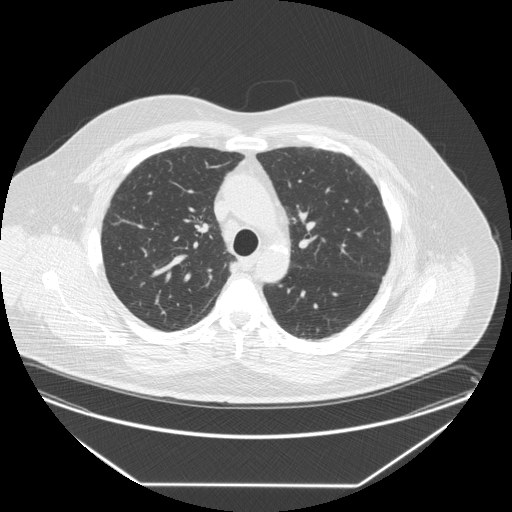
Low-dose screening chest CT, one axial slice; lung window (W 1500 / L -600 HU); 2.5 mm slice thickness; 512 × 512 image matrix, field of view 440 × 440 mm.
Outlined on this slice (manually delineated by an expert):
- lesion 1 (tumor, upper lobe of right lung): bounding box (x1, y1, x2, y2) in pixels: (230, 261, 241, 274)